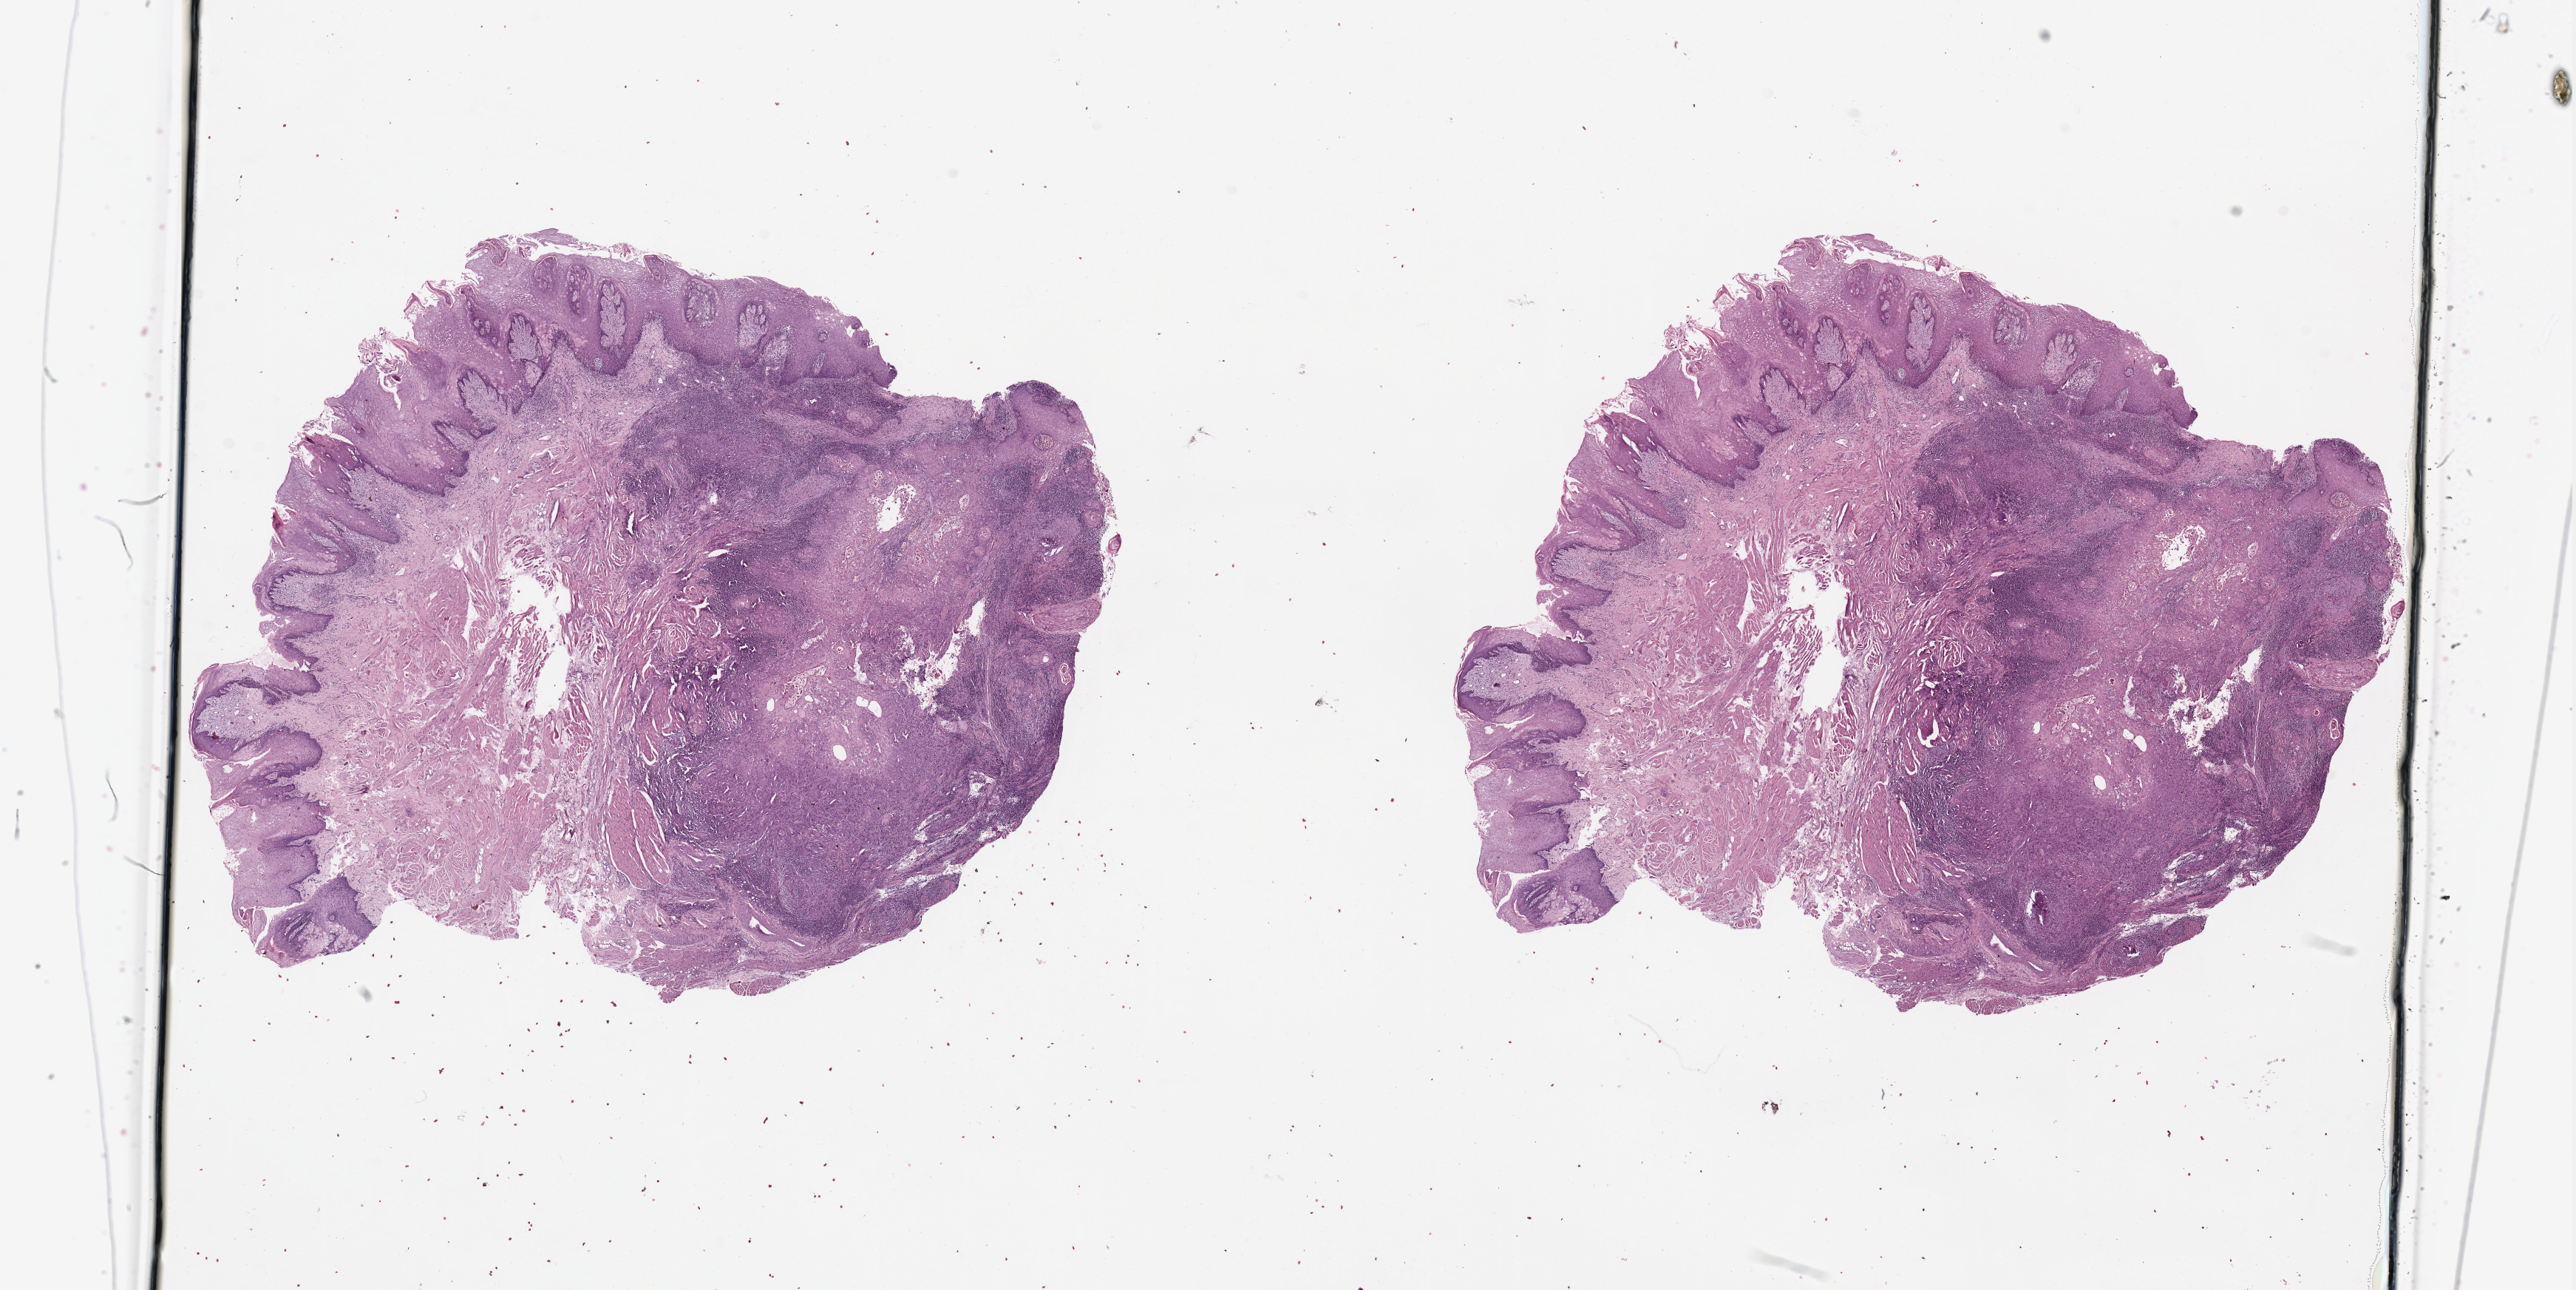
Digitized H&E tissue section (whole slide) — whole scanned area (about 27.6 x 13.8 mm, acquisition: 20x scan) shown as a low-resolution overview; head and neck, tissue type not recorded. Male, 23 y/o.
Patient diagnosis: Squamous cell carcinoma, NOS.